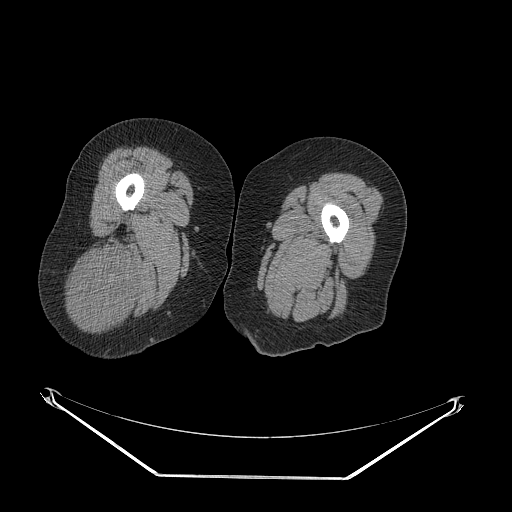
CT of an extremity soft-tissue mass (from a PET/CT study), one axial slice. Slice 33 of 257 in the series (ordered by position). Soft-tissue window (W 400 / L 40 HU). 512 × 512 image matrix, field of view 500 × 500 mm. Female patient. Case-level facts recorded for this patient, not image findings: histological type: synovial sarcoma; grade: intermediate; site of the primary tumour: right buttock.
Outlined on this slice (expert contour drawn on MRI and transferred to this co-registered scan by the dataset authors):
- gross tumour volume including surrounding oedema: bounding box [x1, y1, x2, y2] px = [69, 242, 138, 330]
- gross tumour volume (mass): [69, 247, 138, 330]